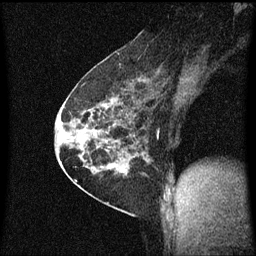
Breast MRI (dynamic contrast-enhanced), one sagittal slice. Slice 37 of 60 in the series (ordered by position). Dynamic contrast-enhanced series, image 2 of 3 at this slice position (ordered by acquisition). 1.5 T. TE 4.2 ms, TR 8.4 ms. 256 × 256 image matrix, field of view 200 × 200 mm. Female patient, age 60 years.
Outlined on this slice (semi-automatically segmented with operator editing):
- analysis volume of interest (the breast-tissue region the enhancement analysis was run in; not a lesion): box from (x=69, y=66) to (x=150, y=193) px
- tumour enhancement mask (voxels above the 70 % enhancement threshold inside the analysis volume of interest): (x=69, y=66)–(x=148, y=175)